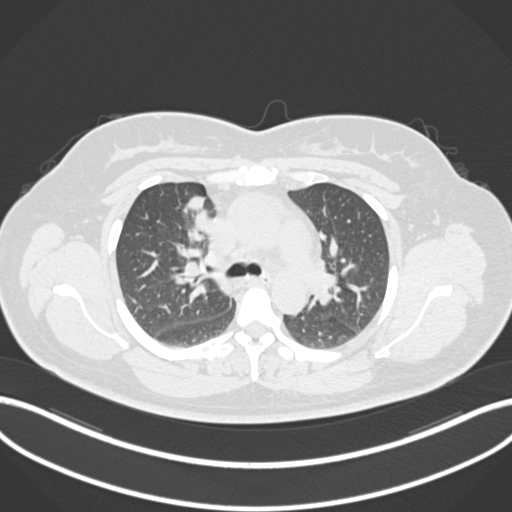
Chest CT, one axial slice; position 120 of 183 along the scan axis; reconstruction kernel B30f; lung window (W 1500 / L -600 HU); 512 × 512 image matrix, field of view 400 × 400 mm. Patient: female, 46 years. Case-level facts recorded for this patient, not image findings: clinical TNM (as recorded): T2a N1 M0.
Outlined on this slice (bounding box drawn by a radiologist):
- lung tumour (recorded histology: adenocarcinoma): bounding box <183,191,209,237> (left, top, right, bottom; pixels)